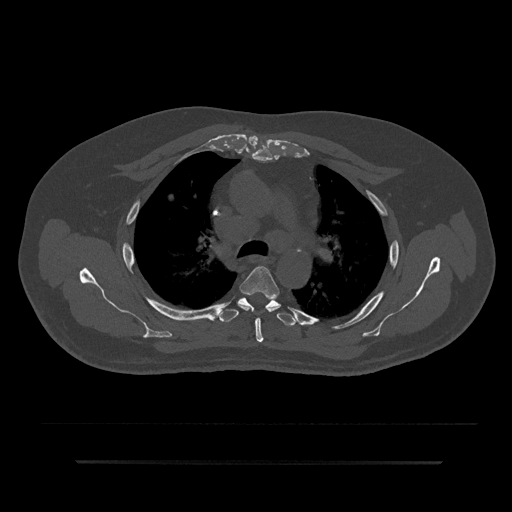
CT including the spine, one axial slice; slice 600 of 797 in the series (ordered by position); bone window (W 1800 / L 400 HU); 0.5 mm slice thickness; 512 × 512 image matrix, field of view 464 × 464 mm. Patient: male, 59 years. From the clinical record (not read from this slice): primary cancer: bile ducts; vertebrae with lytic lesions (as recorded): T10.
Outlined on this slice (semi-automatic segmentation, software-assisted and operator-edited):
- T4 vertebra: bounding box (x1, y1, x2, y2) in pixels: (239, 266, 280, 343)
- T5 vertebra: (219, 297, 298, 326)